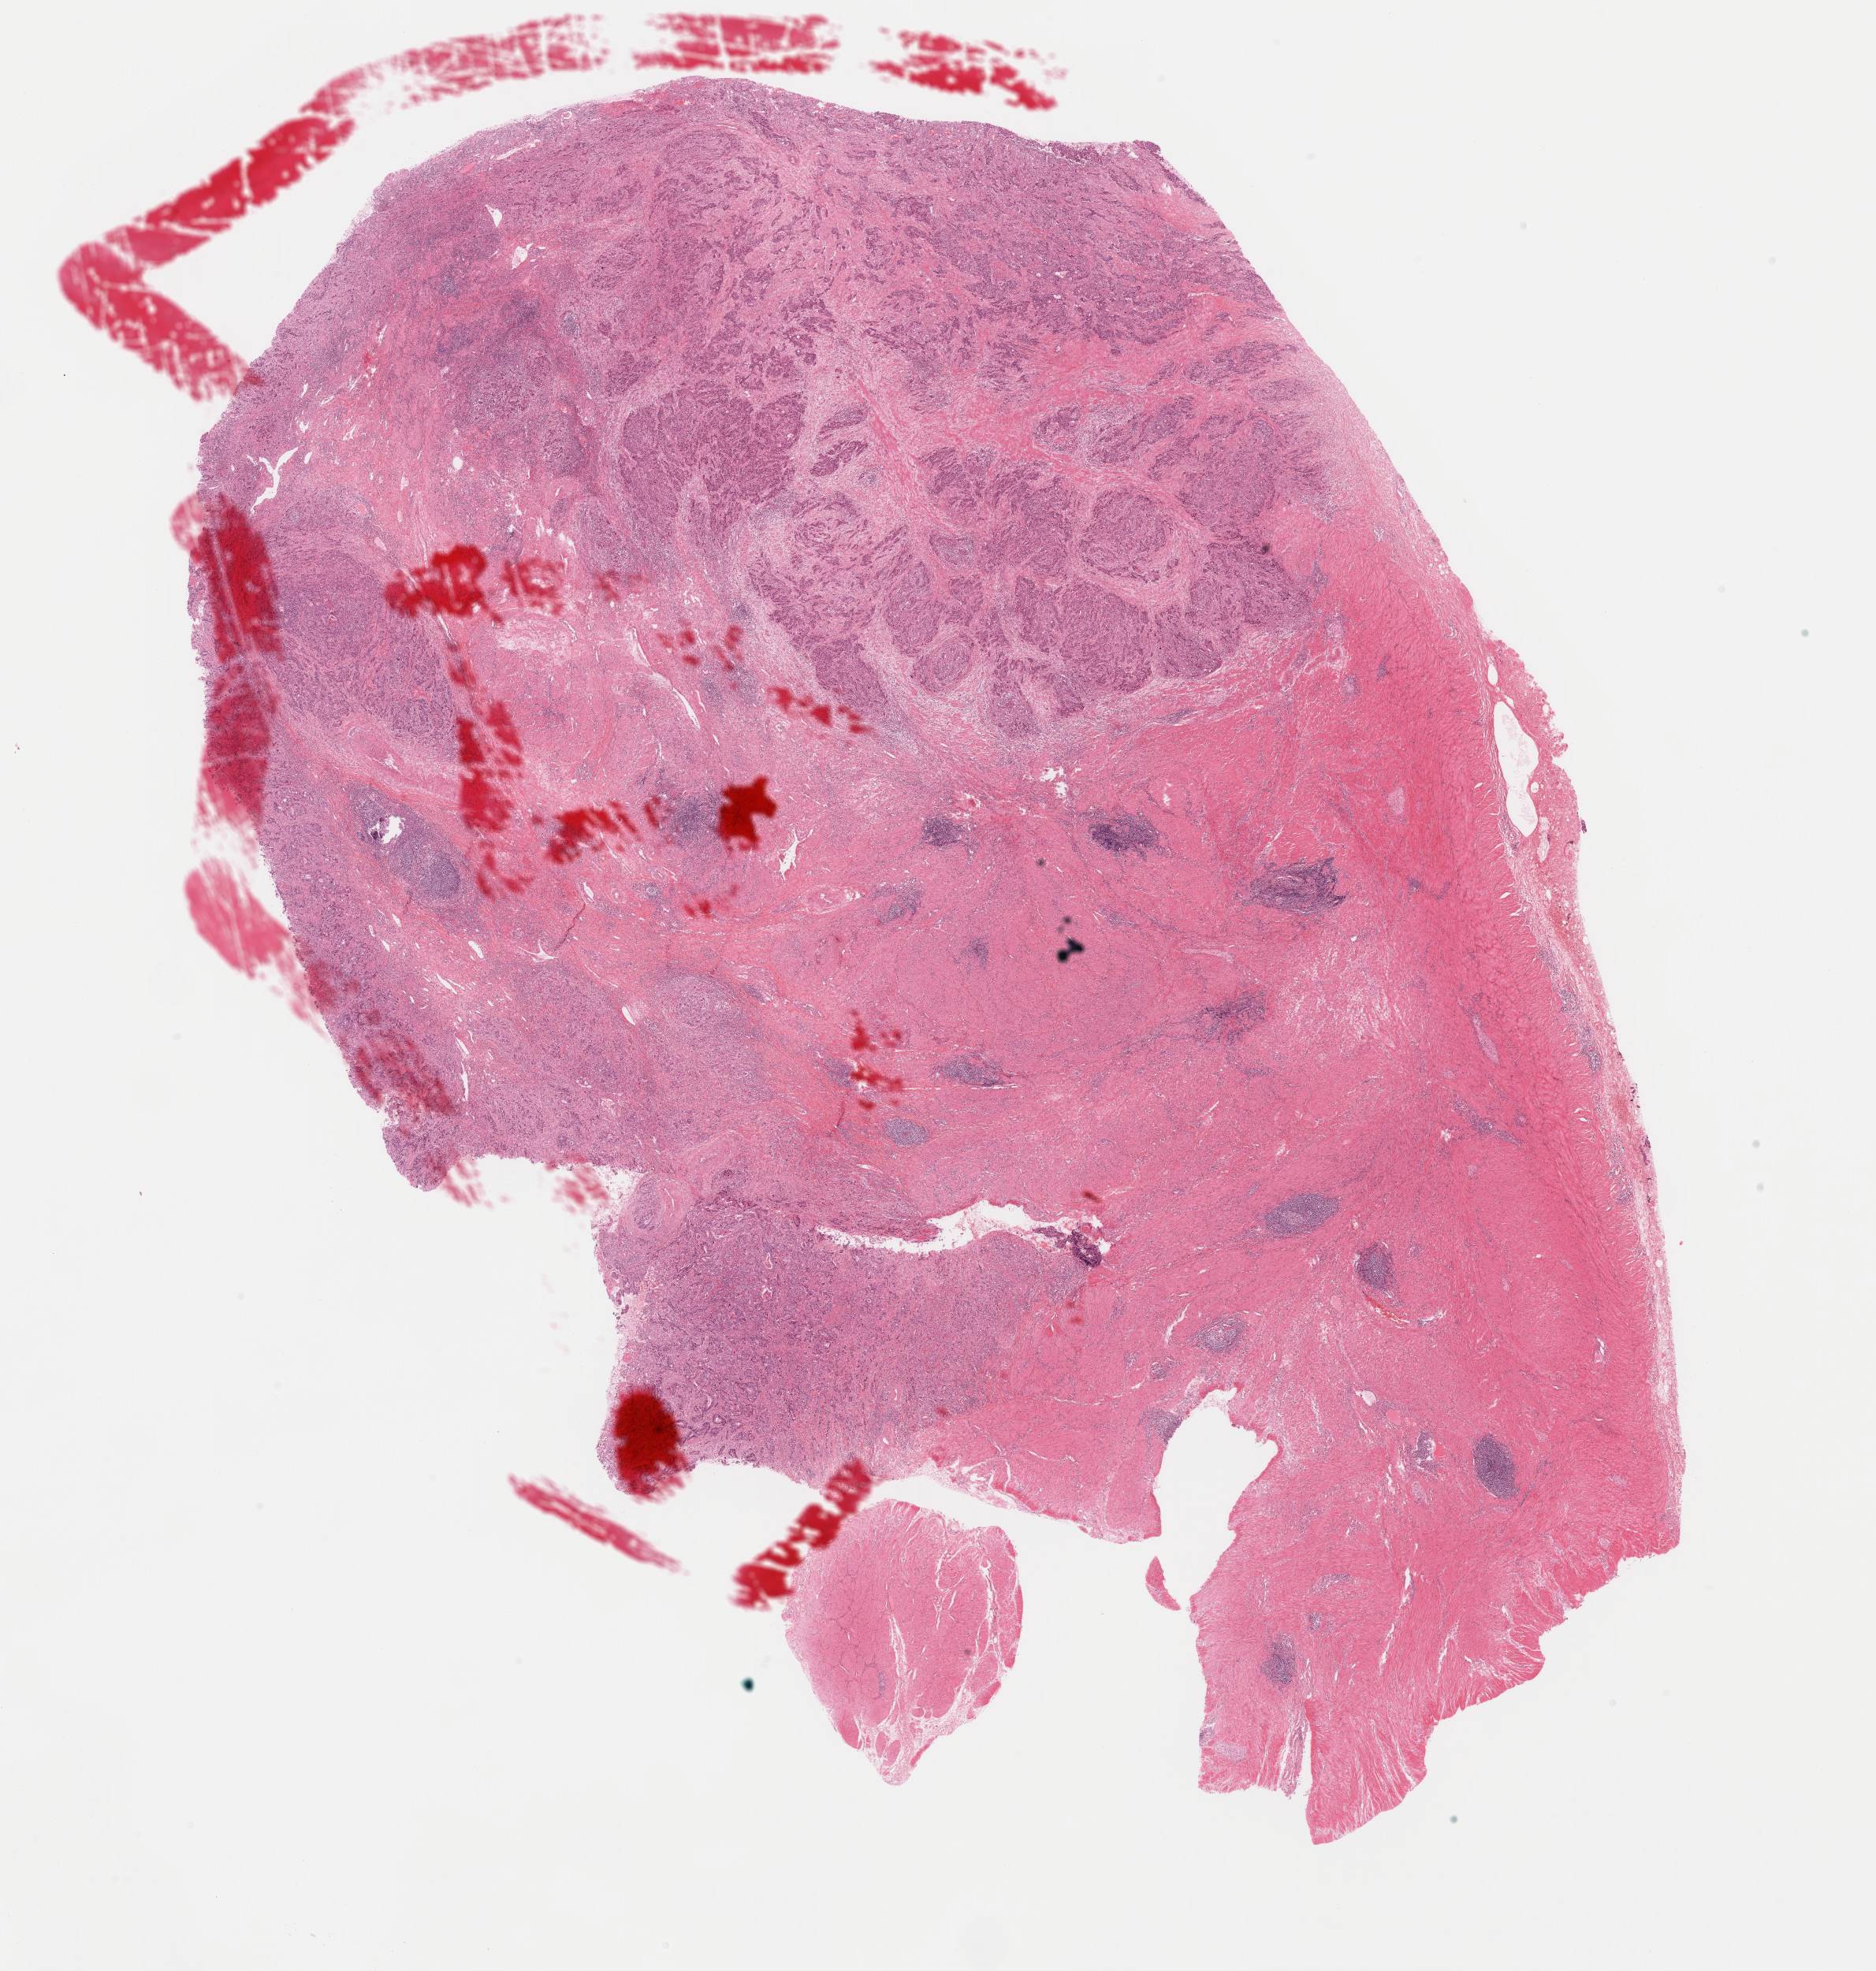
Digitized Hematoxylin and eosin (H&E) stained tissue section (whole slide) — whole scanned area (about 18.8 x 19.8 mm, acquisition: 40x scan) shown as a low-resolution overview; FFPE section; primary tumour sample from the stomach. Female patient; age at initial diagnosis 70 years. Histologic grade: G3 (poorly differentiated).
* TNM: T3 N0 M0
* AJCC pathologic stage: IIA (7th edition)
* histologic diagnosis: Adenocarcinoma, NOS (gastric antrum)